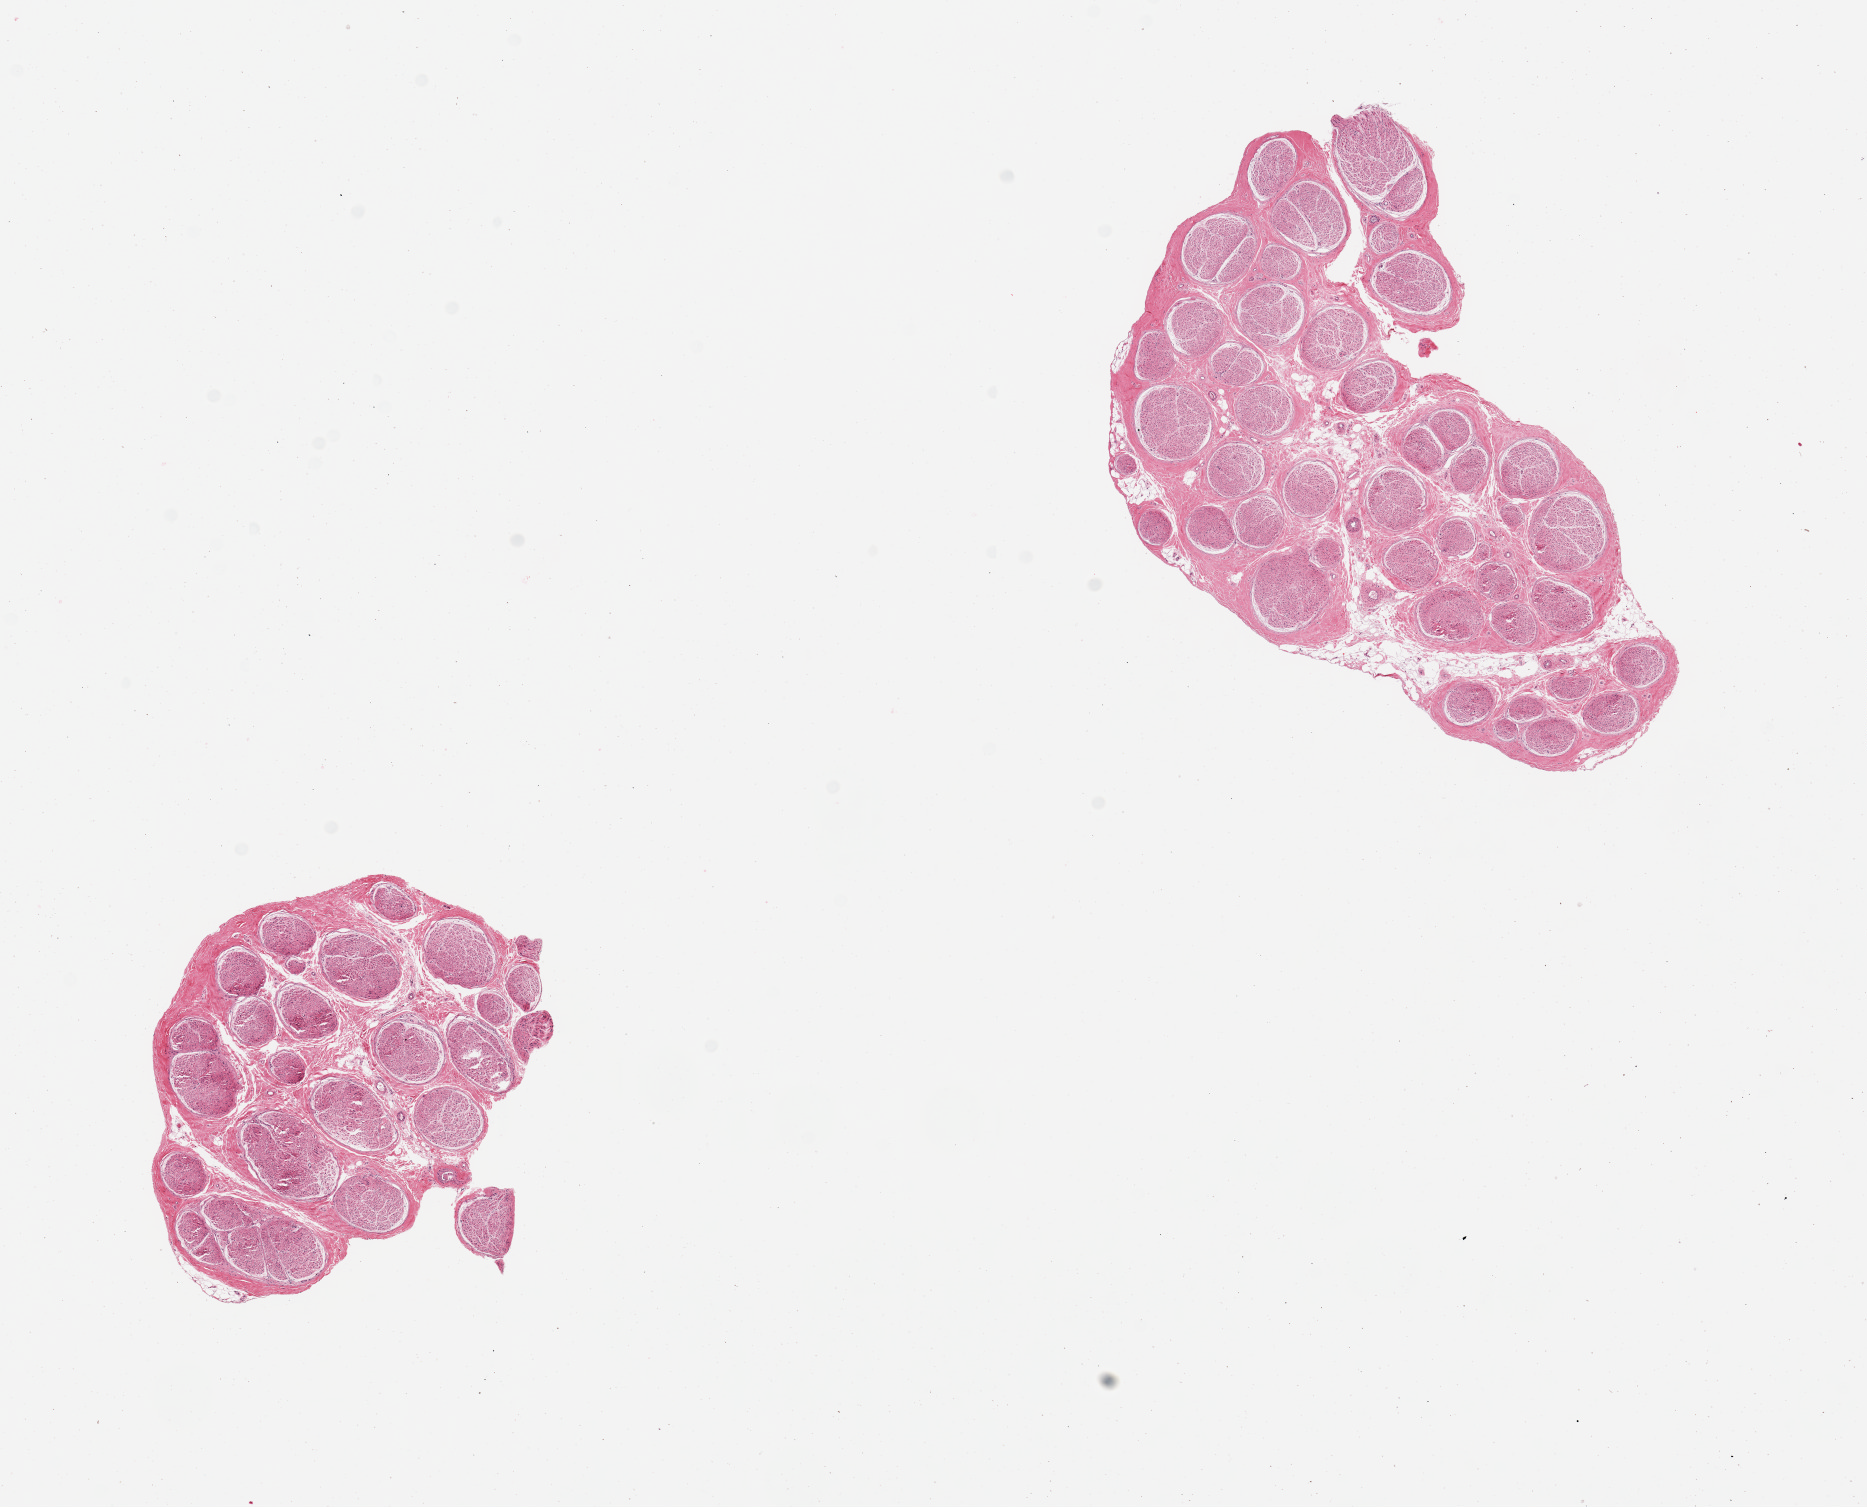
Digitized H&E-stained section, shown as a low-resolution overview of the whole scanned area (about 14.8 x 11.9 mm), PAXgene-fixed paraffin-embedded (PFPE) section, target tissue: tibial nerve, donor tissue sample. Donor: male.
• pathologist's review note for this sample: 2 pieces, excellent clean specimens